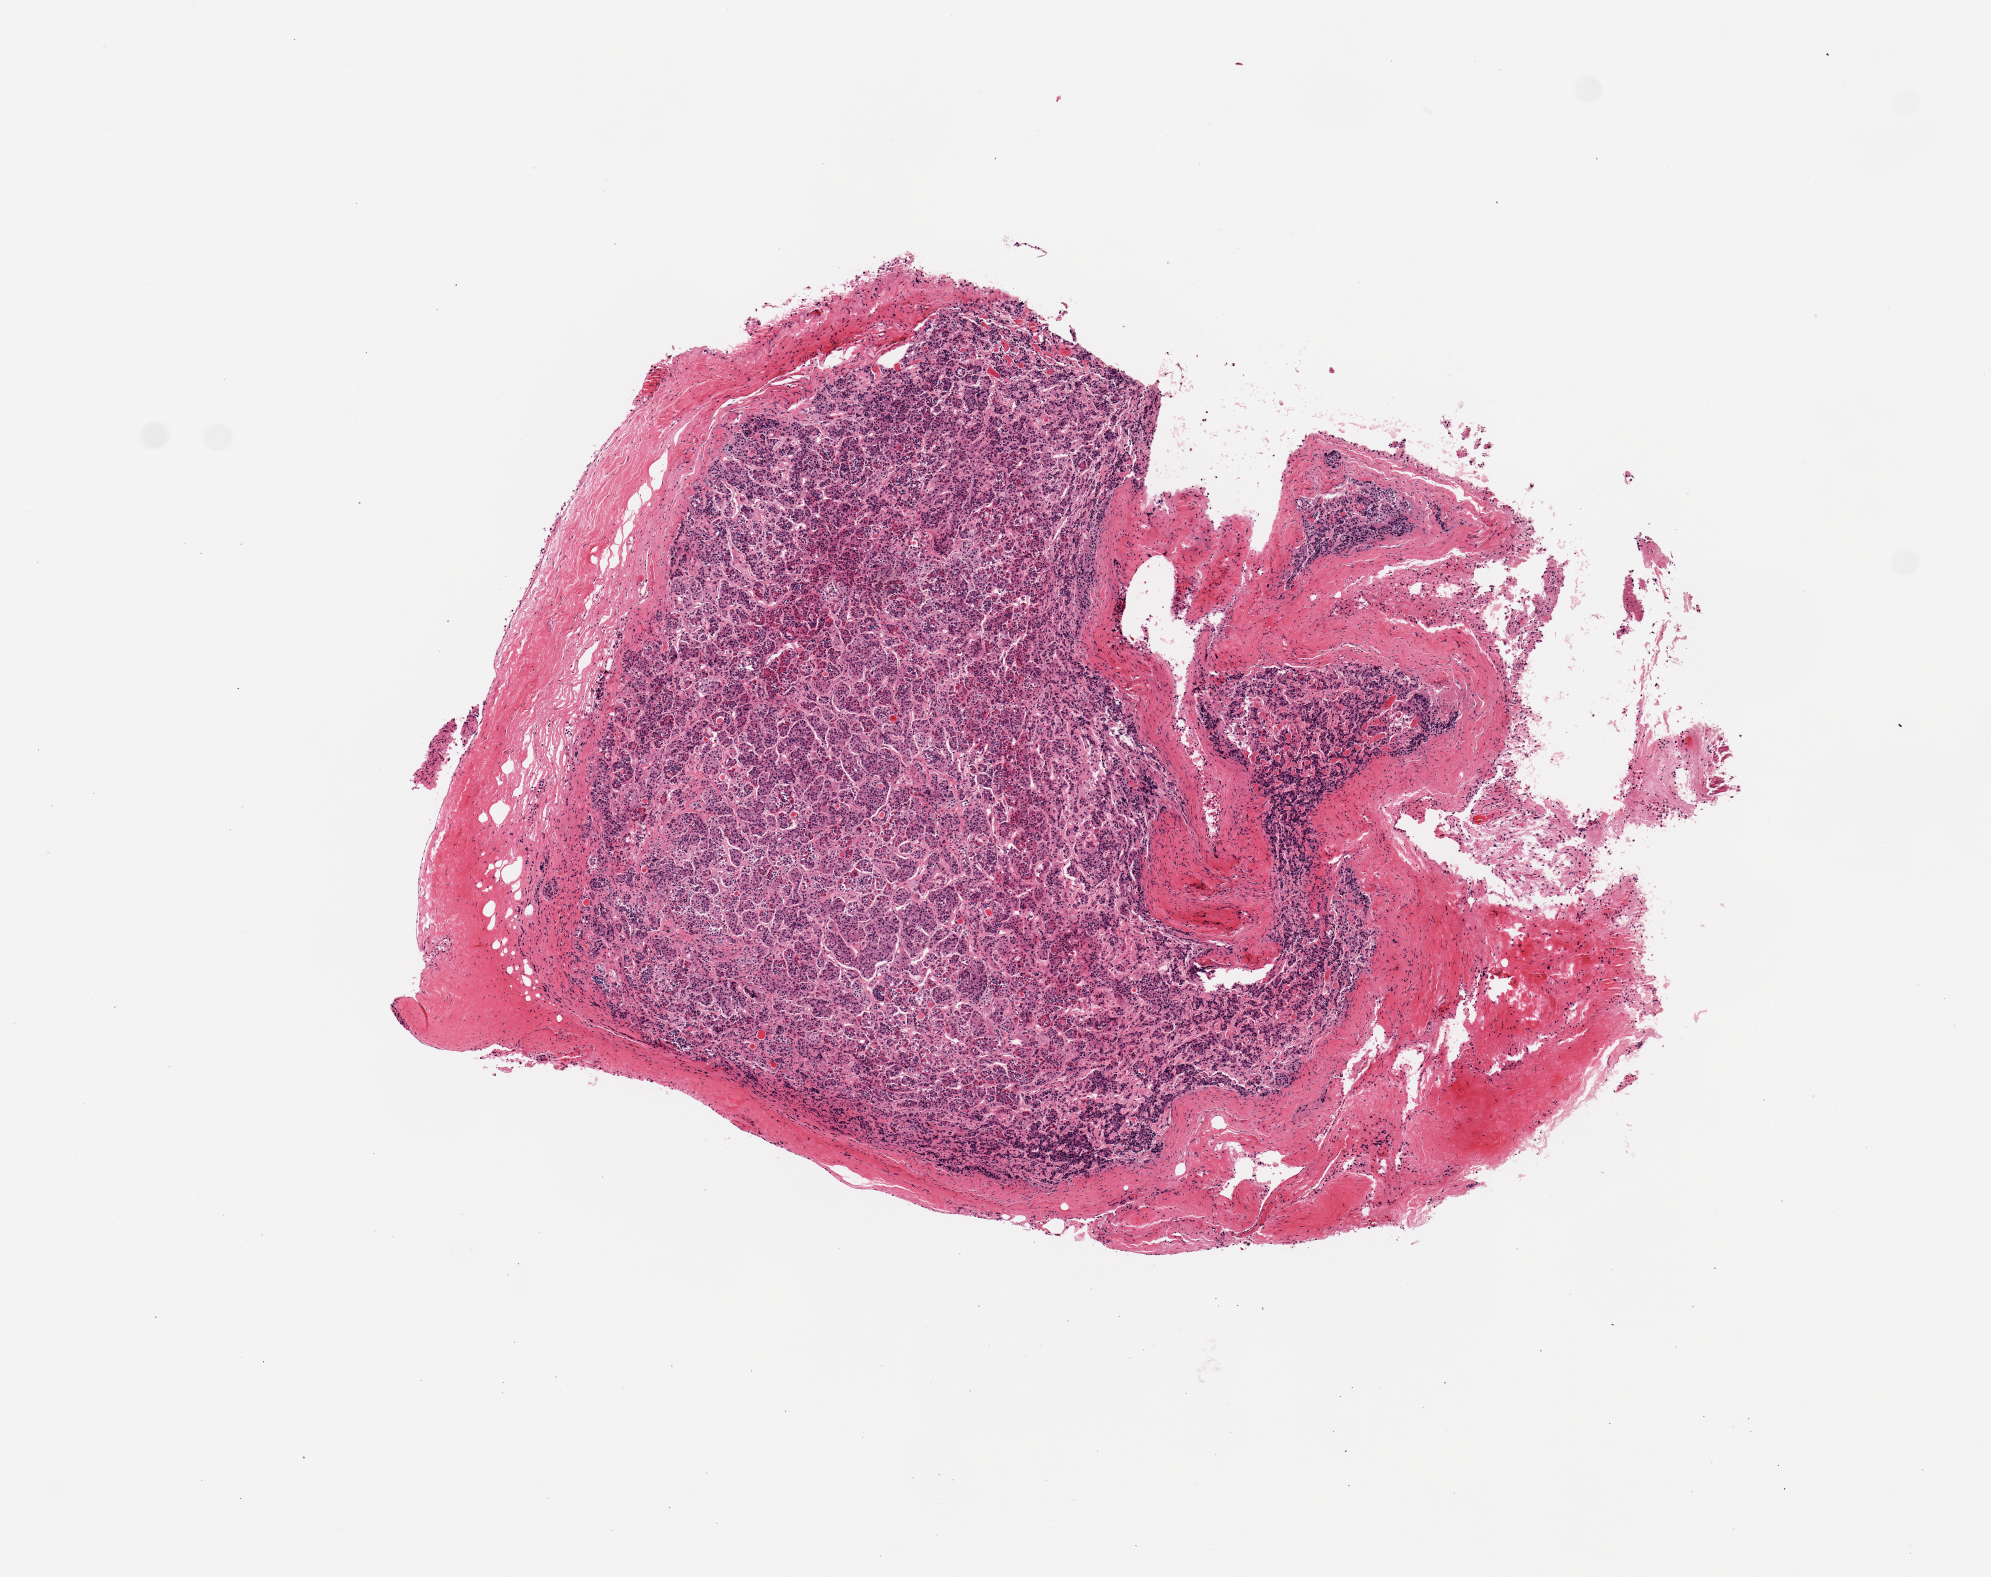
Whole-slide image, haematoxylin and eosin stain — shown as a low-resolution overview of the whole scanned area (about 7.9 x 6.2 mm); PAXgene-fixed paraffin-embedded (PFPE) section; sampled site (target tissue): pituitary; donor tissue sample. Donor: male.
Pathologist's review note for this sample: 1 piece, ~30% dura--rest is adenohypophysis.